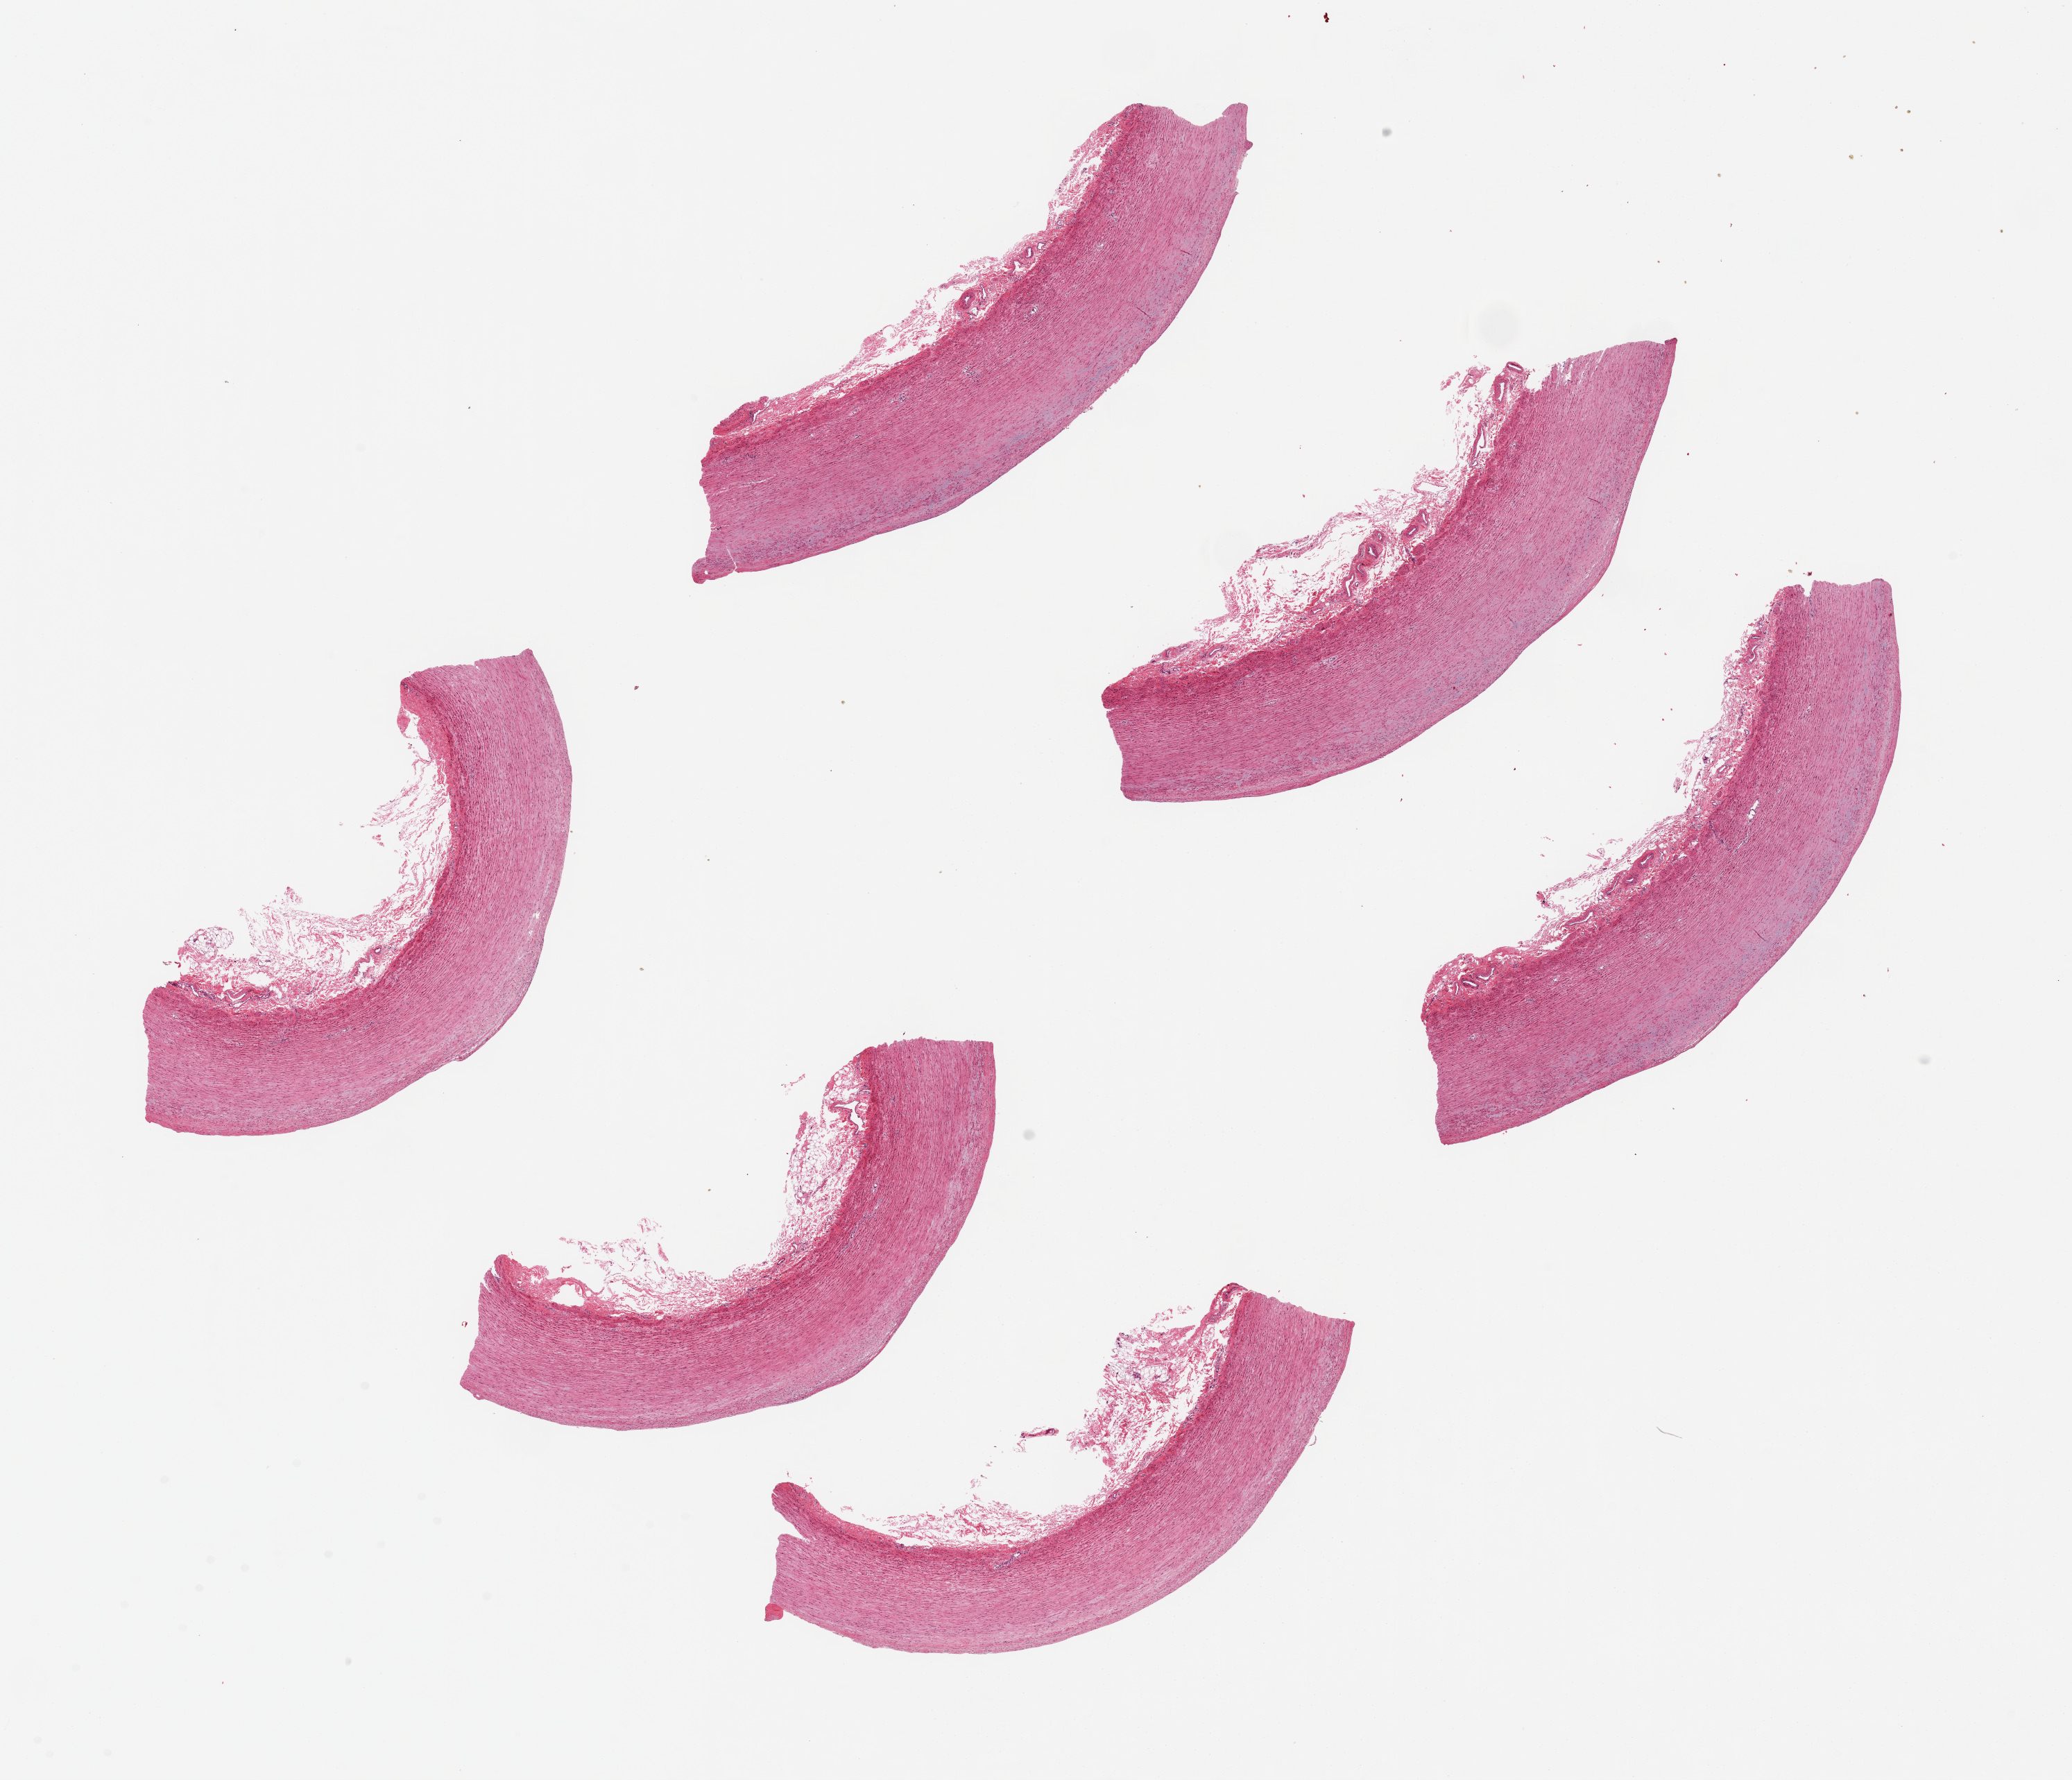
Whole-slide image, H&E stain — low-resolution overview of the scanned area, about 23.6 x 20.3 mm (slide scanned at 20x). PAXgene-fixed, paraffin-embedded tissue. Section of aorta (target tissue). Donor tissue sample. Female donor.
Review note (as recorded): 6 pieces, ~ 7.5x1.5mm. Vasa vasorum well-demonstrated.